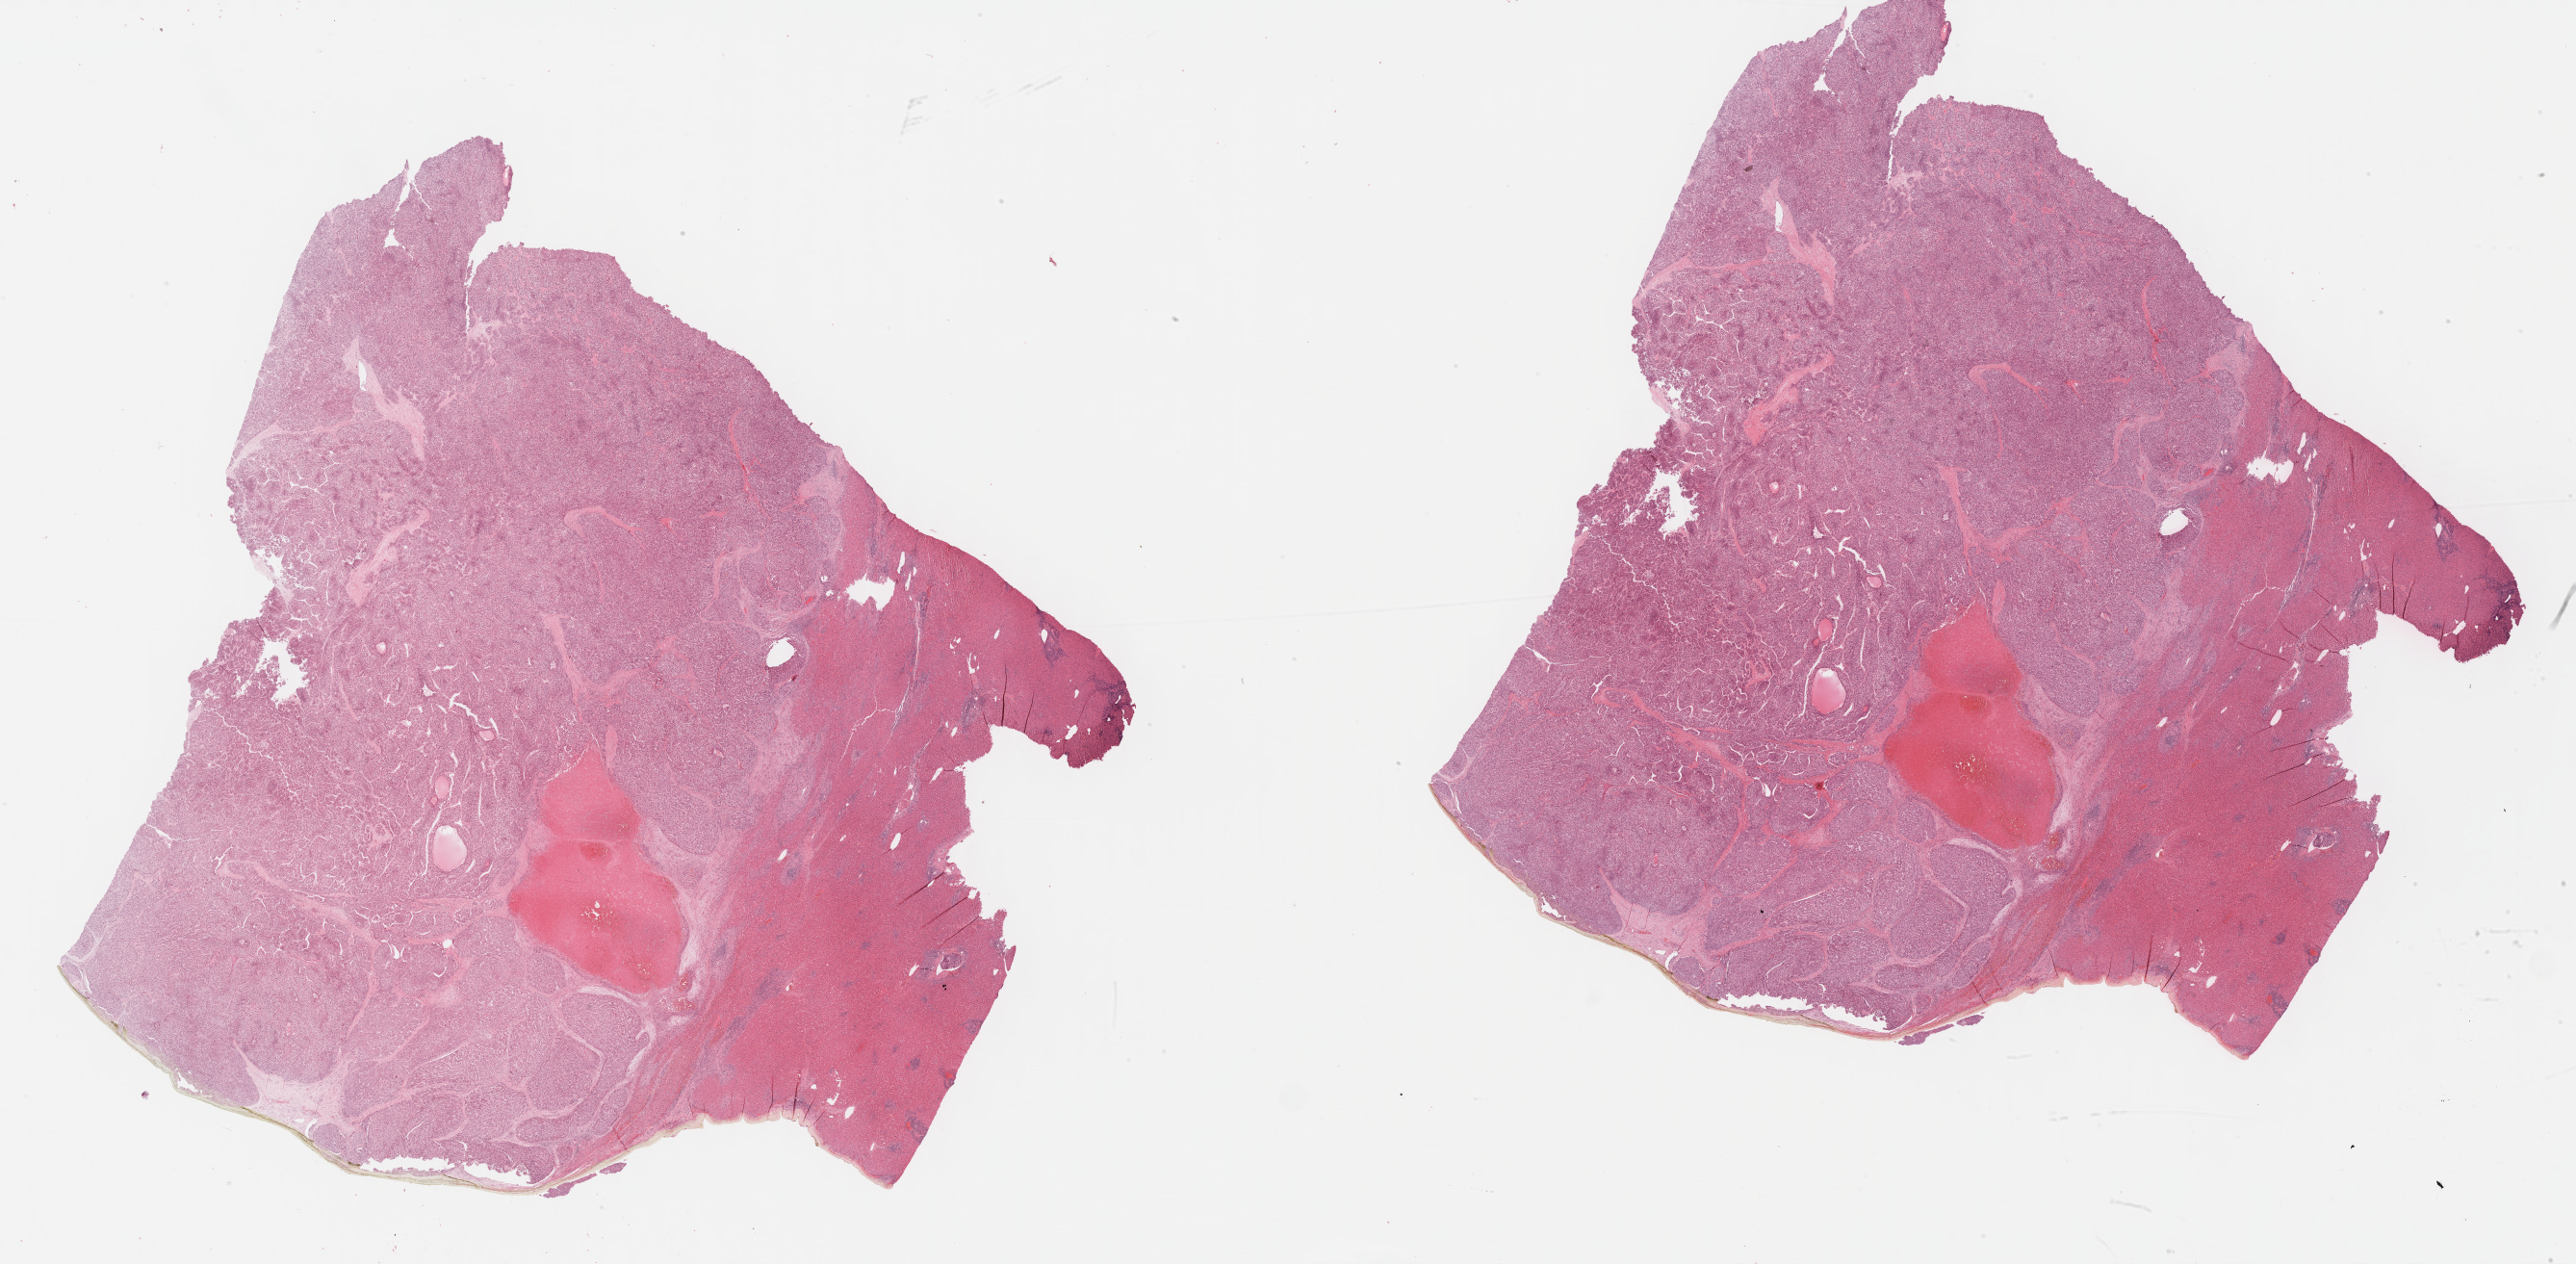
Whole-slide histology image, Hematoxylin and eosin (H&E) stained, whole scanned area (about 43.3 x 21.2 mm, acquisition: 40x scan) shown as a low-resolution overview, formalin-fixed paraffin-embedded (FFPE) diagnostic section, liver, primary tumour sample. Male patient; age at initial diagnosis 73 years. Histologic grade: G3 (poorly differentiated).
* histologic diagnosis: Hepatocellular carcinoma, NOS
* AJCC pathologic stage: II (6th edition)